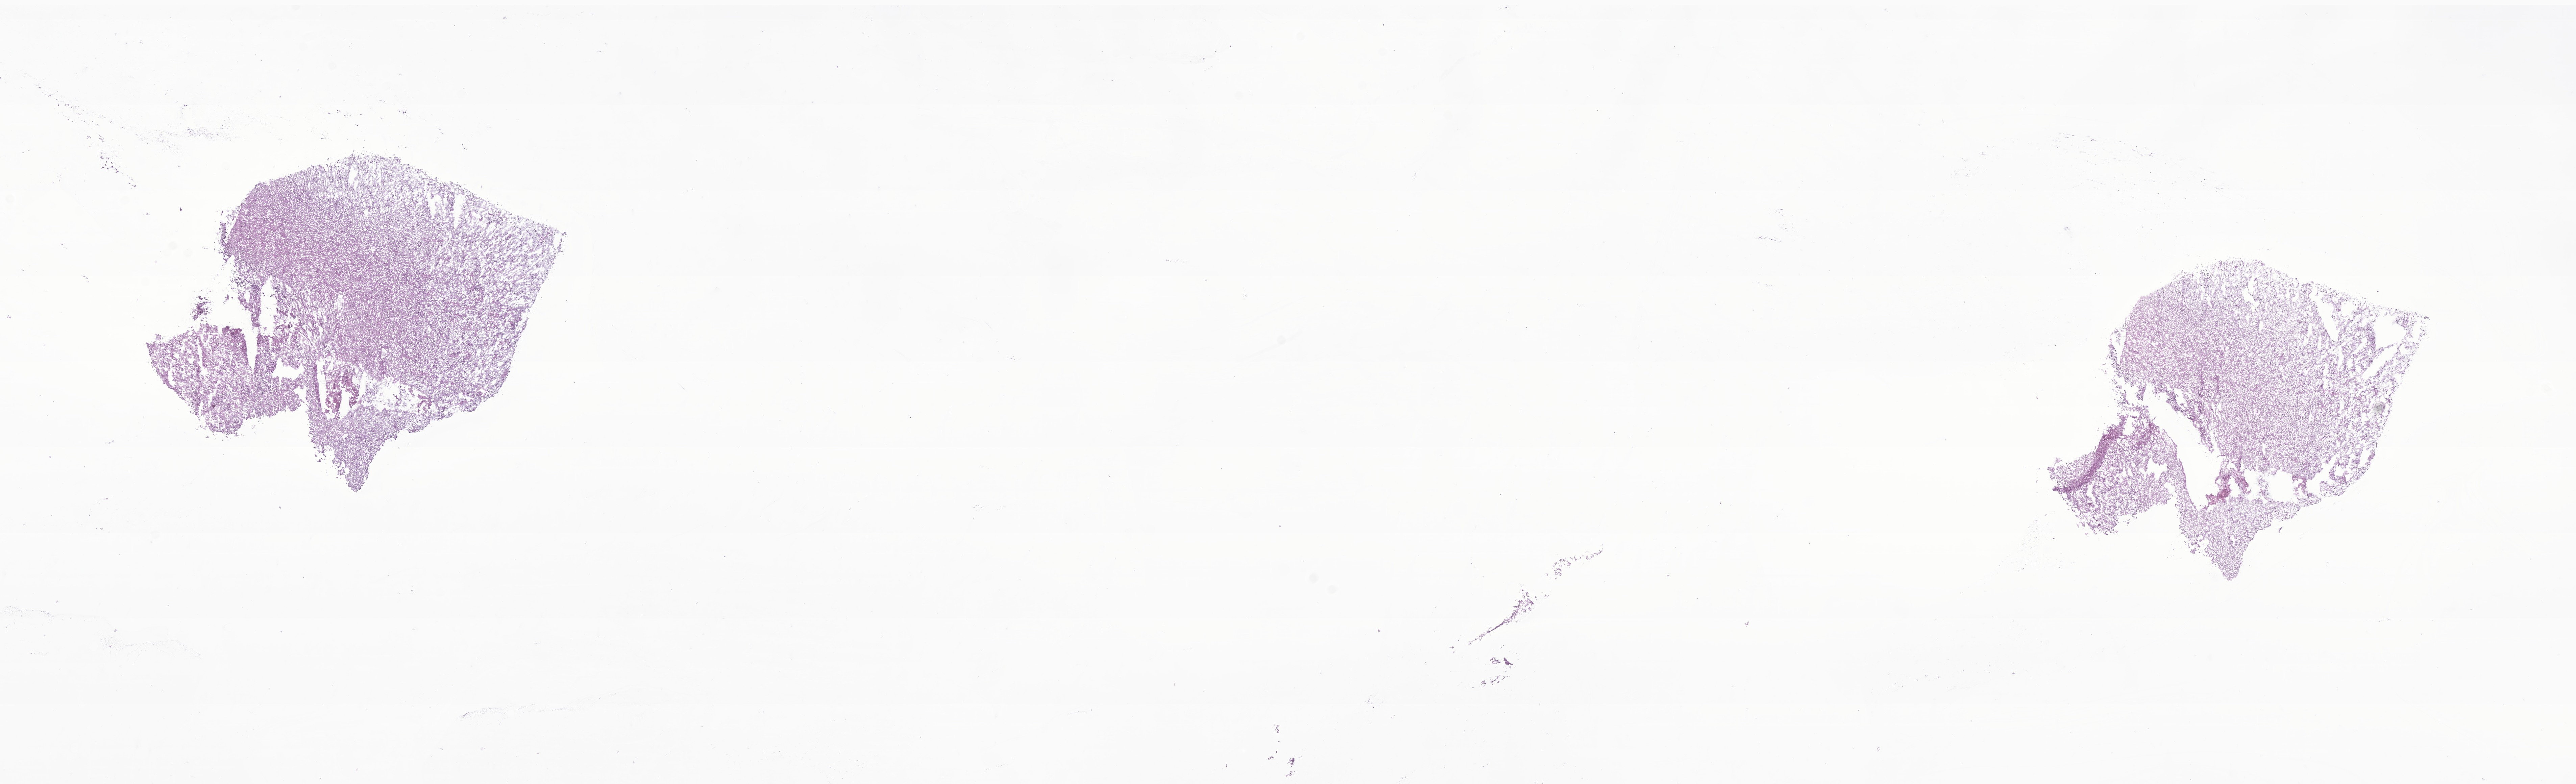
H&E whole-slide image of tumor tissue from the cerebellum, whole scanned area (about 32.1 x 9.8 mm) shown as a low-resolution overview; cryosection (OCT / tissue freezing medium). Female patient, age 124 months (10 years 4 months).
Diagnosis: Neoplasm, uncertain whether benign or malignant.